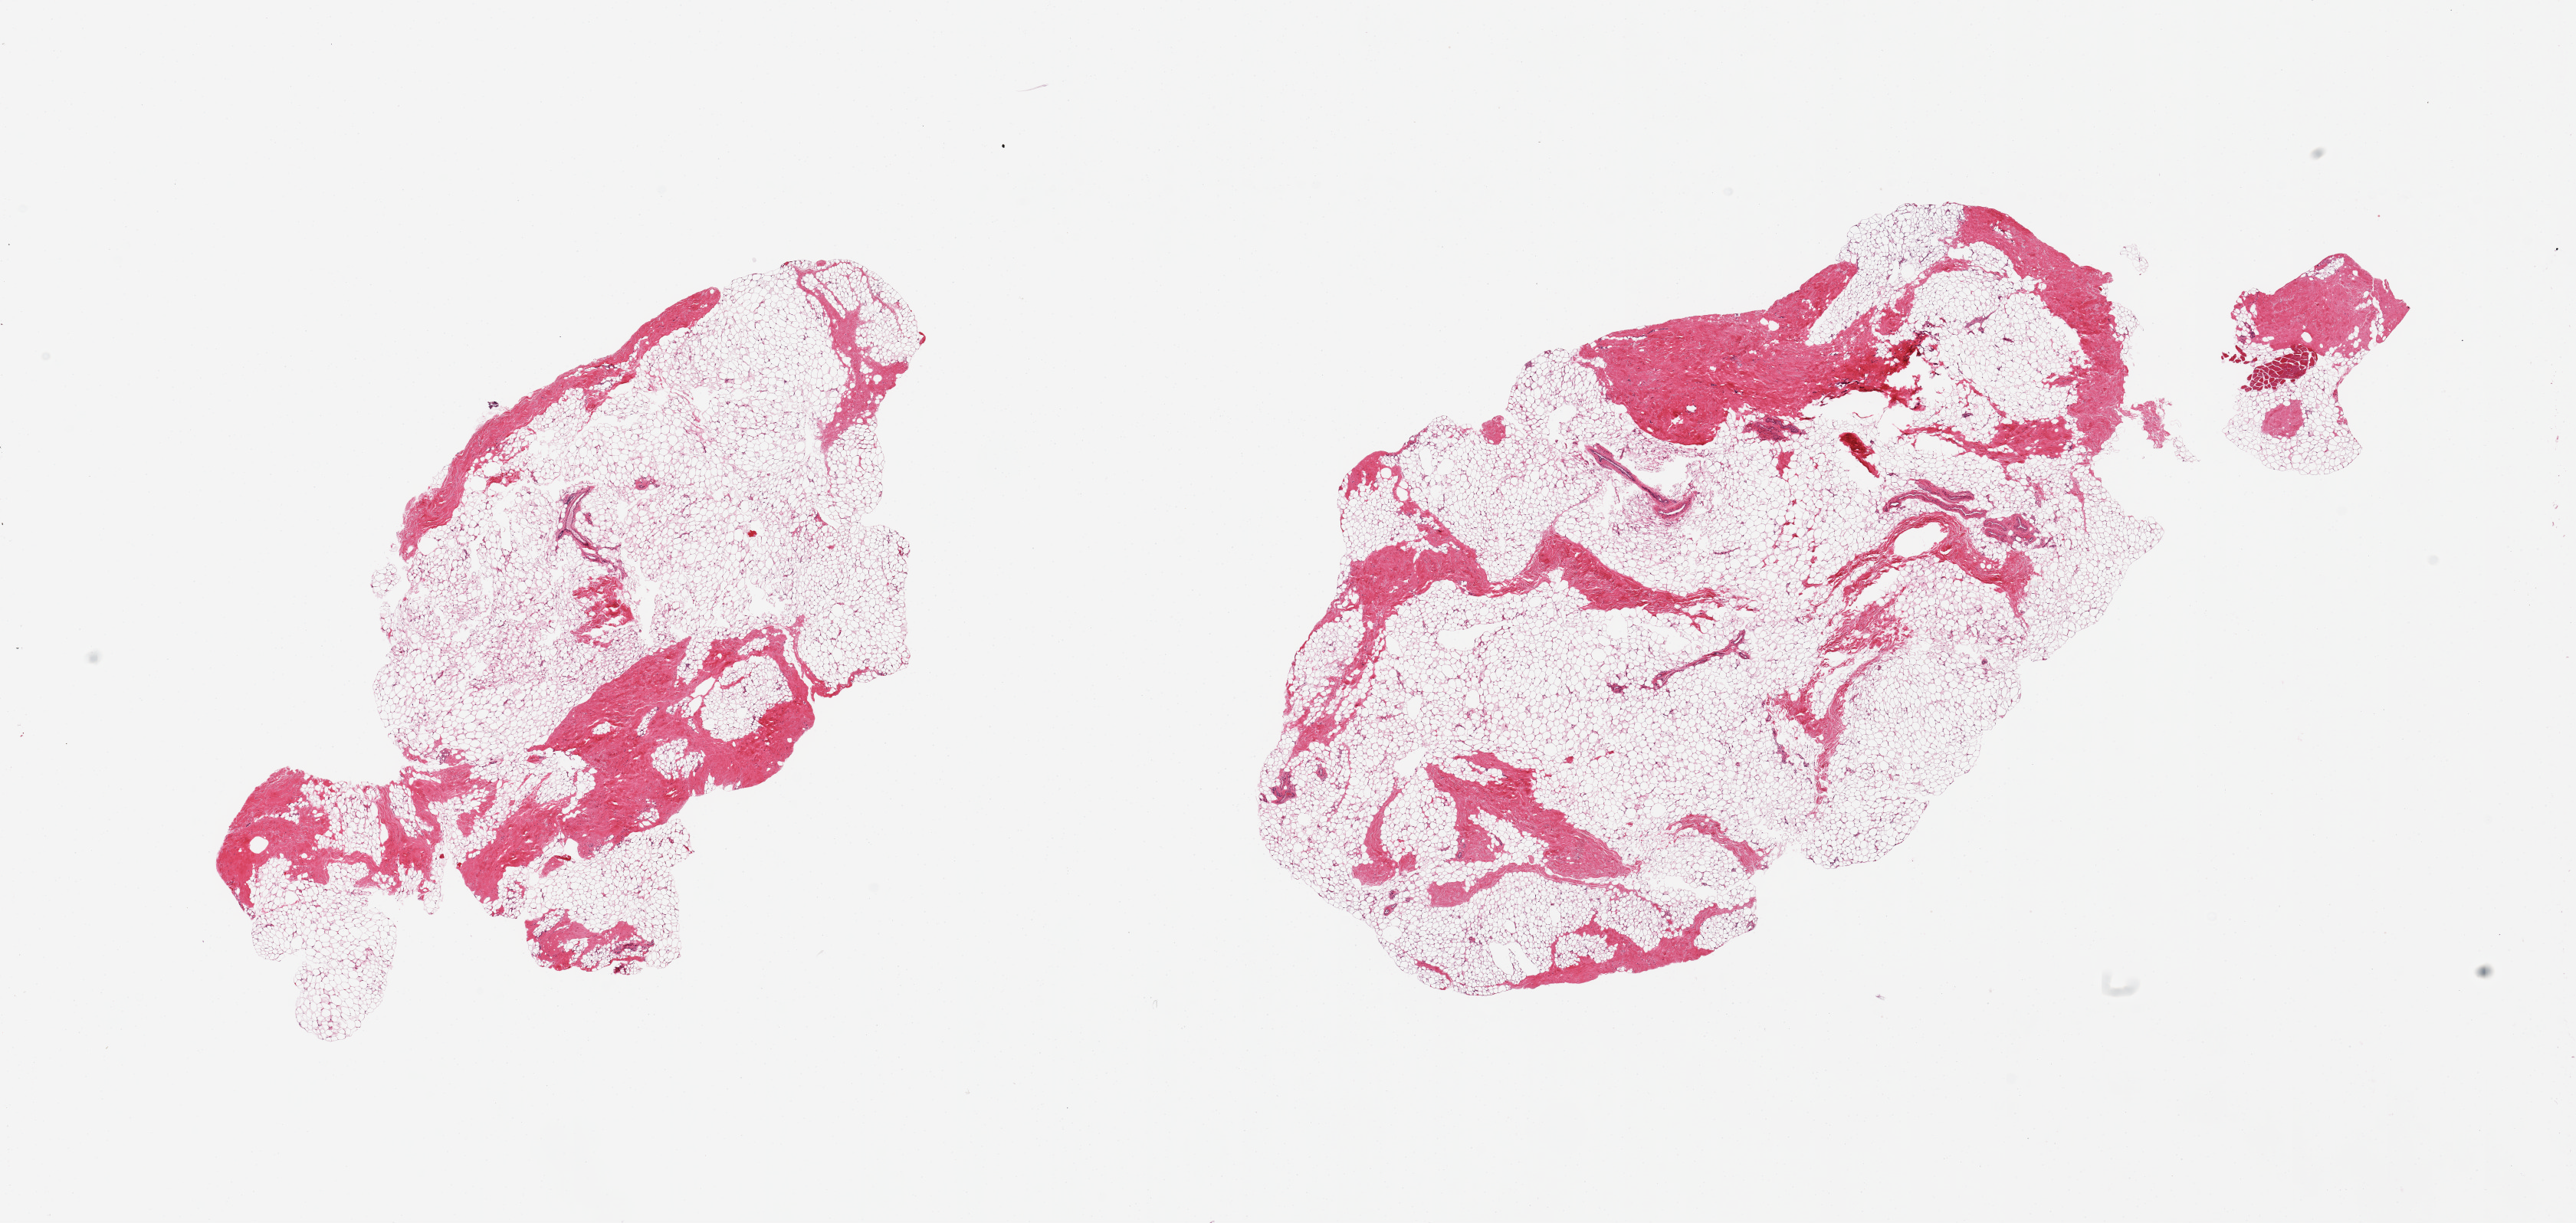
Hematoxylin and eosin (H&E) whole-slide image — shown as a low-resolution overview of the whole scanned area (about 26.6 x 12.6 mm), PAXgene-fixed, paraffin-embedded tissue, target tissue: breast, donor tissue sample. Donor sex: male.
Pathologist's review note for this sample: 2 pieces, fibroadipose elements only.